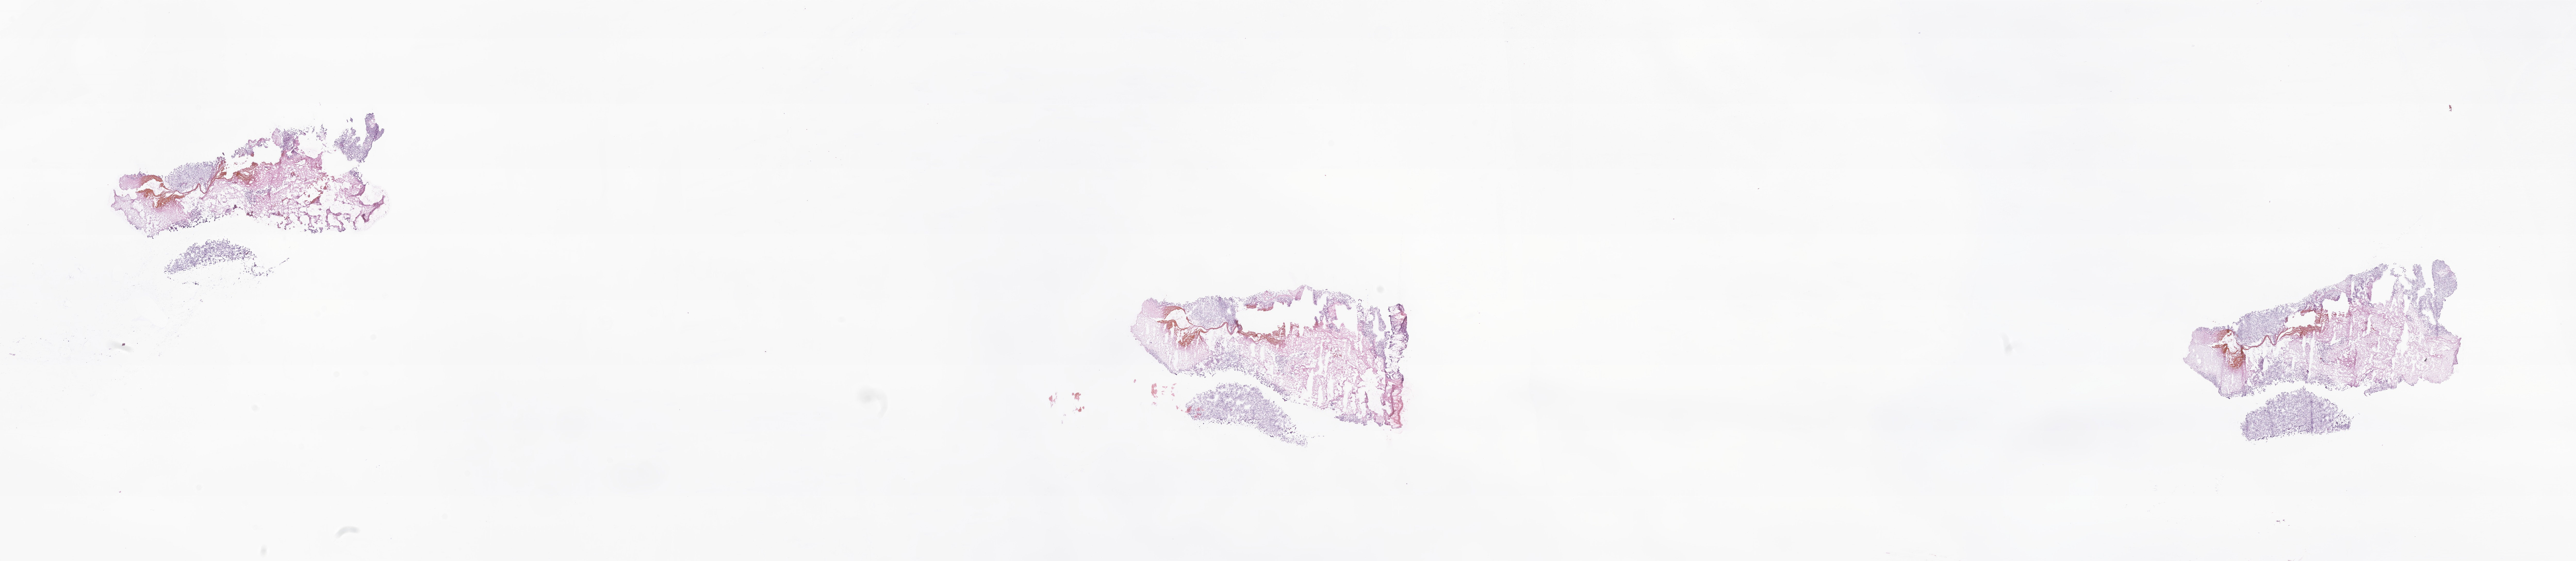
Hematoxylin and eosin (H&E) whole-slide image of tumor tissue from the cerebellum — shown as a low-resolution overview of the whole scanned area (about 42.1 x 9.2 mm), frozen section (OCT-embedded). Patient: male, age 98 days.
• recorded diagnosis: Atypical teratoid/rhabdoid tumor